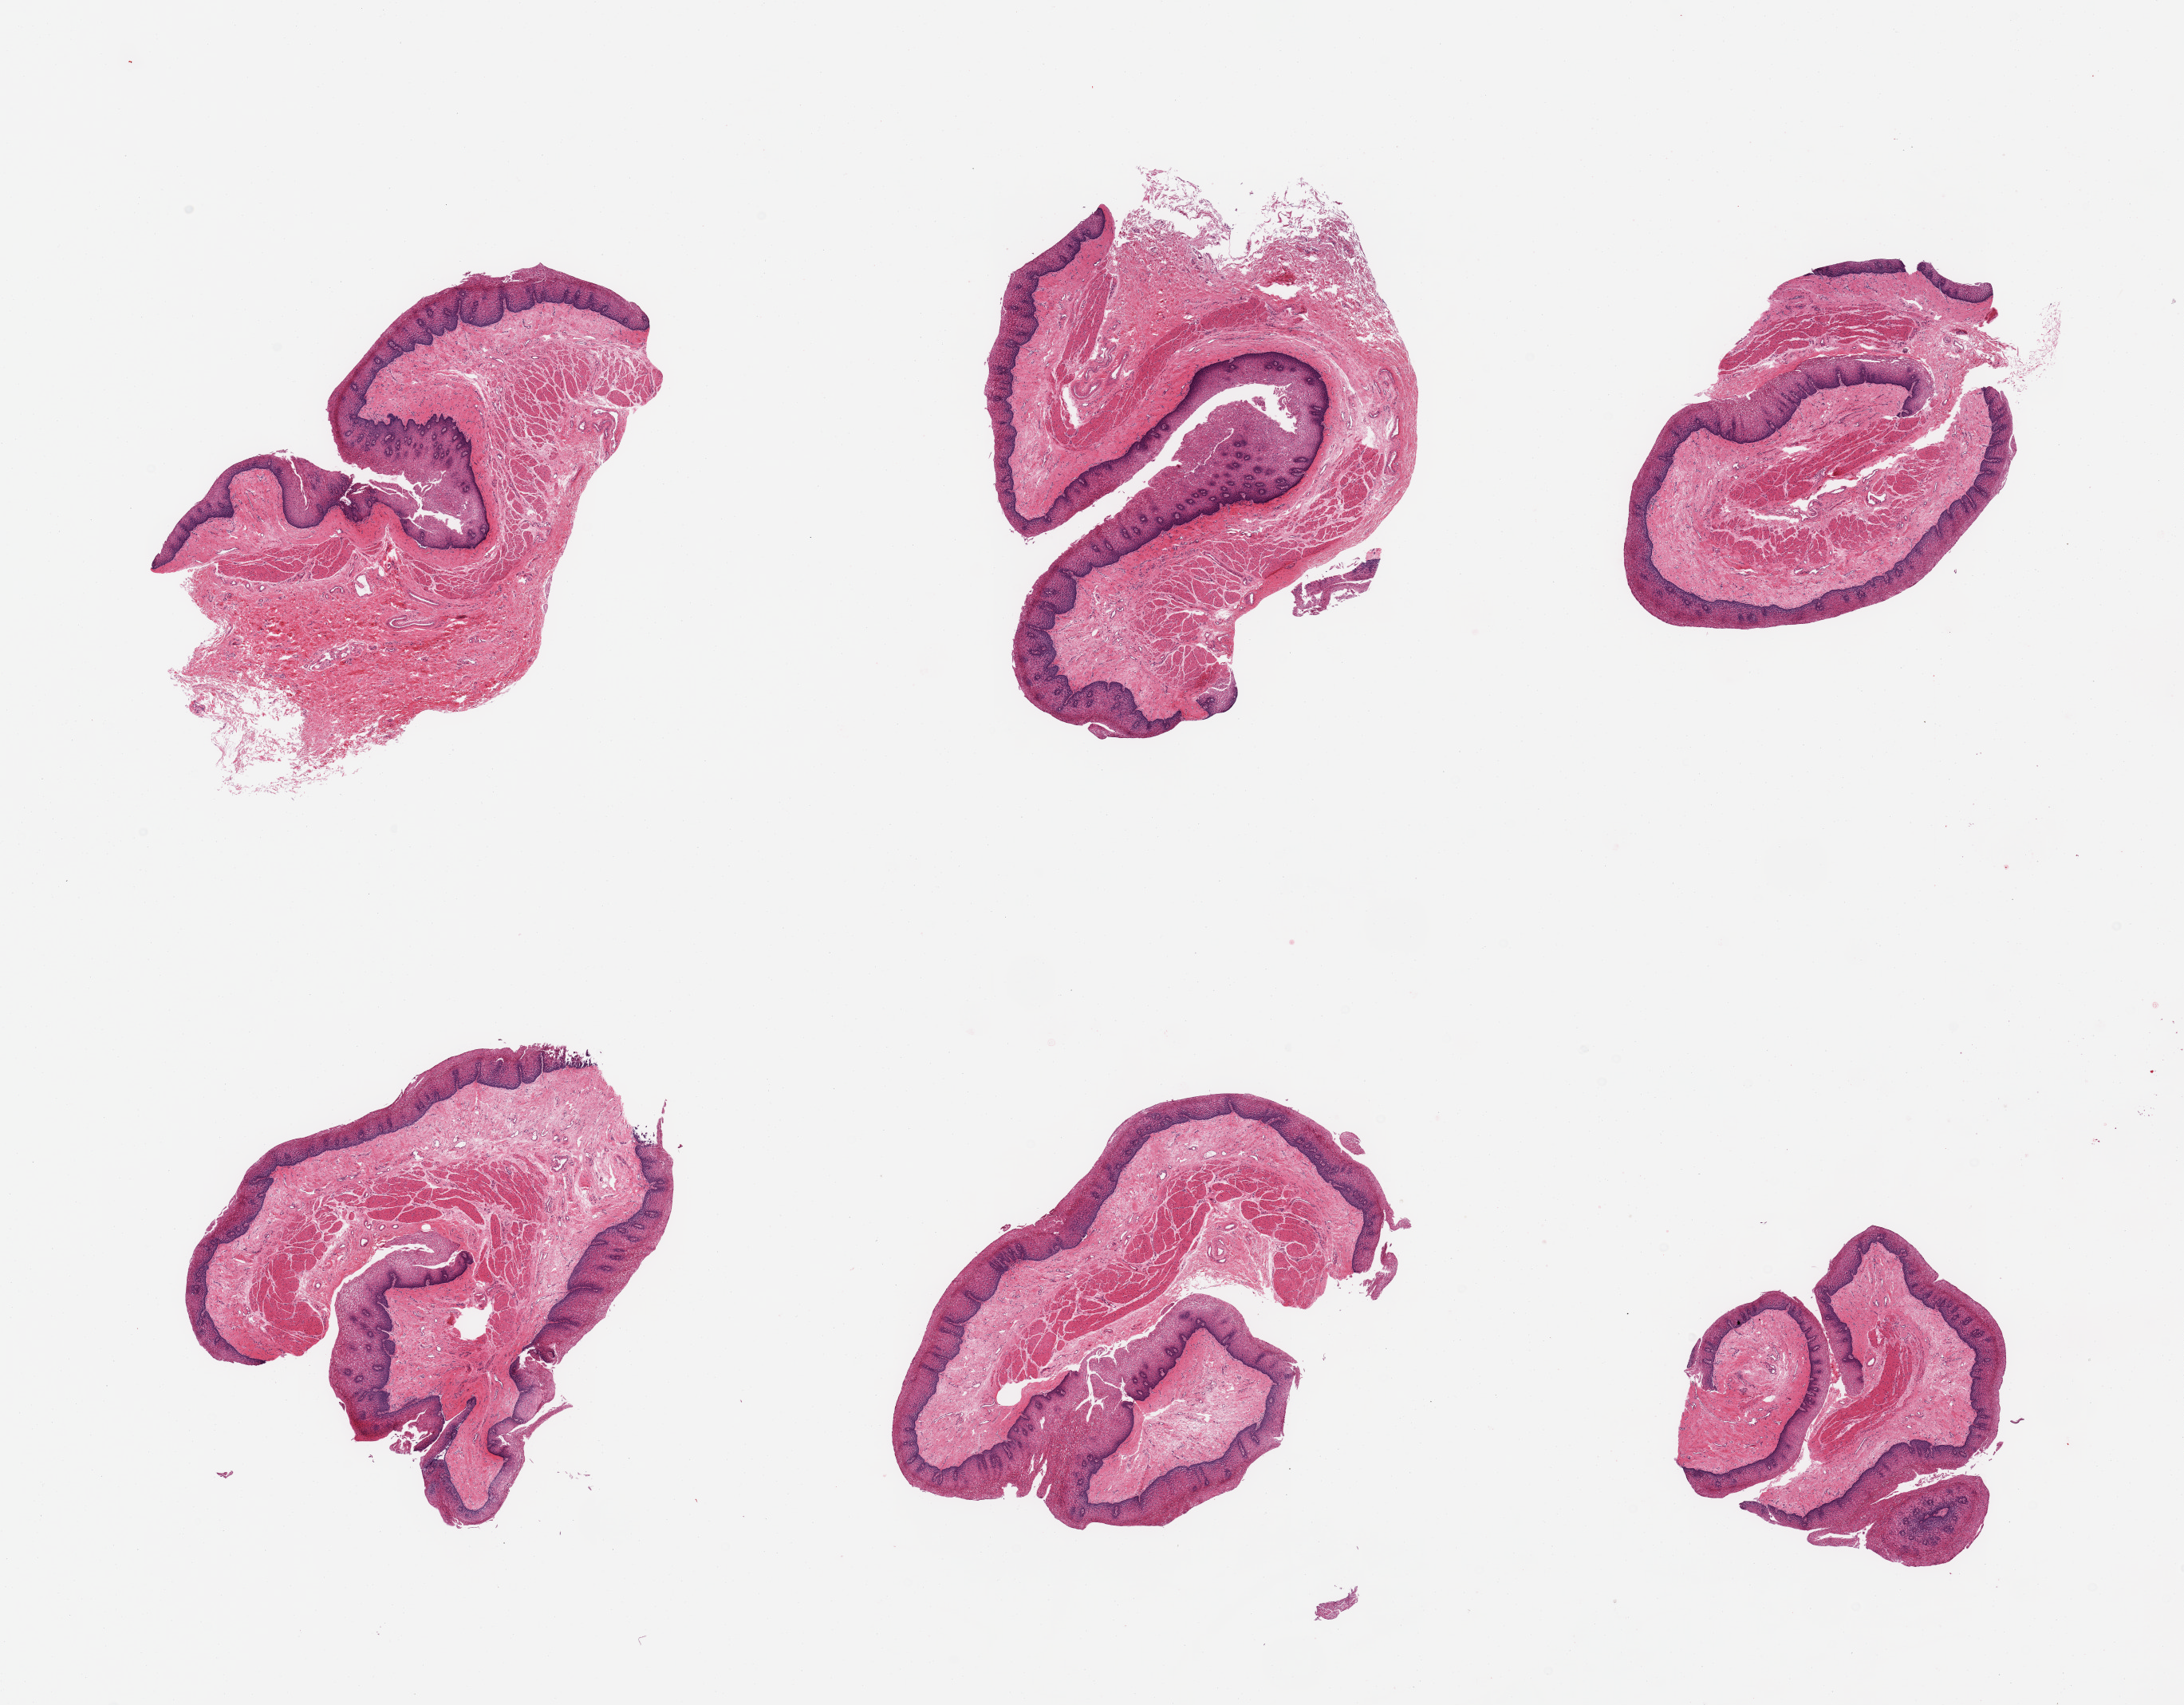
Whole-slide image, hematoxylin and eosin (H&E) stain — low-resolution overview of the scanned area, about 21.7 x 16.9 mm (slide scanned at 20x); PAXgene-fixed, paraffin-embedded tissue; target tissue: esophageal mucous membrane; tissue donor sample.
Review note (as recorded): 6 pieces.